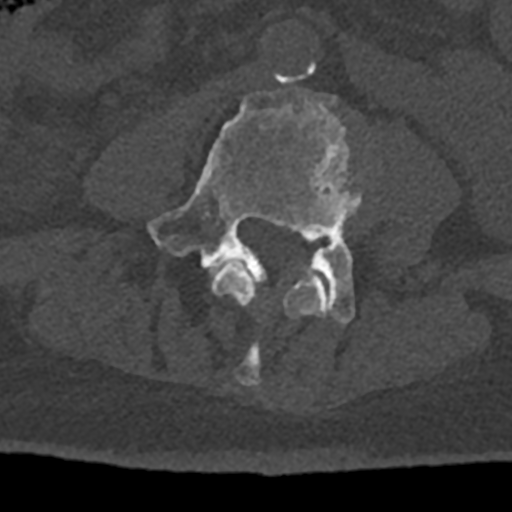
CT including the spine, one axial slice; slice 276 of 797 in the series (ordered by position); 120 kVp; bone window (W 1800 / L 400 HU); 0.5 mm slice thickness; 512 × 512 image matrix, field of view 160 × 160 mm. Male patient, age 74 years. Case-level facts recorded for this patient, not image findings: primary cancer: renal.
Structures marked on this image (semi-automatically segmented with operator editing):
- L3 vertebra: bounding box (x1, y1, x2, y2) in pixels: (211, 260, 330, 386)
- L4 vertebra: (147, 88, 365, 324)